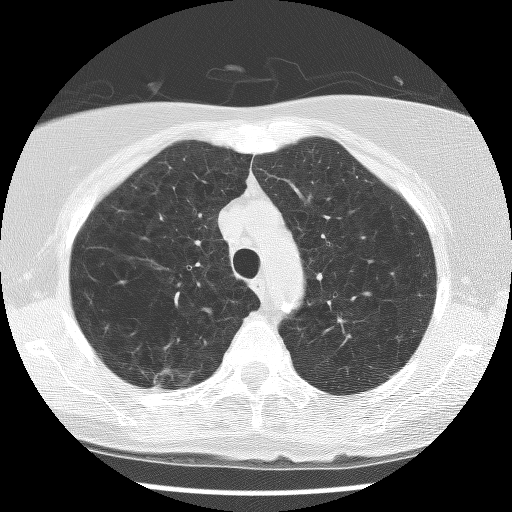
Axial slice from a low-dose chest CT screening exam. First (baseline) screen. Lung window (W 1500 / L -600 HU). 2.5 mm slice thickness. Lung (sharp) reconstruction kernel (BONE). 120 kVp. Slice 33 of 129 in the series. 512 × 512 image matrix, field of view 310 × 310 mm. Female participant, aged 63 years at enrolment.
Expert-annotated lung lesion, bounding box <132,351,193,402> (left, top, right, bottom; pixels). Screening reader's record for this exam (one nodule recorded; not confirmed to be the boxed lesion): non-calcified nodule or mass ≥4 mm, right upper lobe, 9 × 6 mm, spiculated (stellate) margins, mixed attenuation. Official screen result: positive, change unspecified: nodule(s) >= 4 mm or enlarging nodule(s), mass(es), or other non-specific abnormalities suspicious for lung cancer.